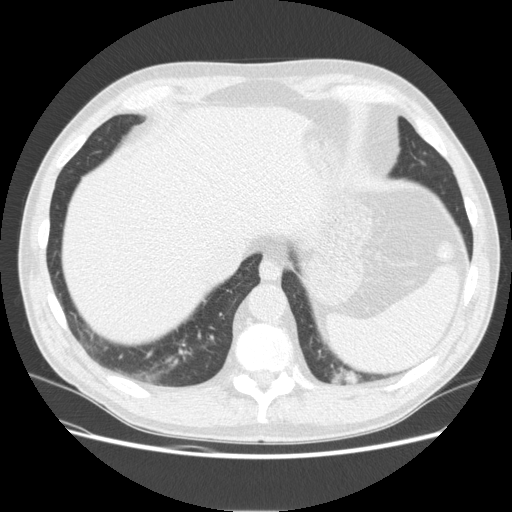
Low-dose screening chest CT, one axial slice; position 43 of 165 along the scan axis; reconstruction kernel STANDARD; lung window (W 1500 / L -600 HU); 512 × 512 image matrix, field of view 375 × 375 mm.
Annotated regions visible in this slice (manually delineated by an expert):
- lesion 1 (tumor, upper lobe of left lung): bounding box <332,367,360,385> (left, top, right, bottom; pixels)